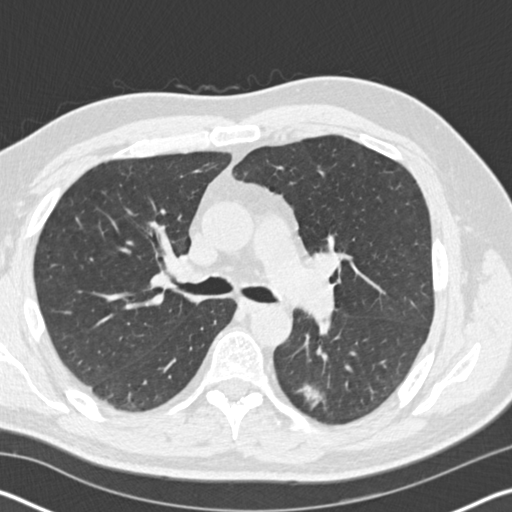
Low-dose screening chest CT, axial slice, baseline screening round, lung window (W 1500 / L -600 HU), 2 mm slice thickness, standard (soft-tissue) reconstruction kernel (B30f), slice 72 of 178 in the series. Male, age 60 years at enrolment. Current smoker at enrolment.
- Expert reader's lesion annotation, box from (x=275, y=367) to (x=357, y=426) px.
- The screening reader recorded 3 non-calcified nodules or masses ≥4 mm on this exam; which of them this box marks is not recorded.
- Official screen result: positive, change unspecified: nodule(s) >= 4 mm or enlarging nodule(s), mass(es), or other non-specific abnormalities suspicious for lung cancer.
- Participant outcome: lung cancer diagnosed 171 days after this screen — papillary adenocarcinoma, NOS, left lower lobe, moderately differentiated (G2), stage IB (AJCC 6th edition), 35 mm at pathology.